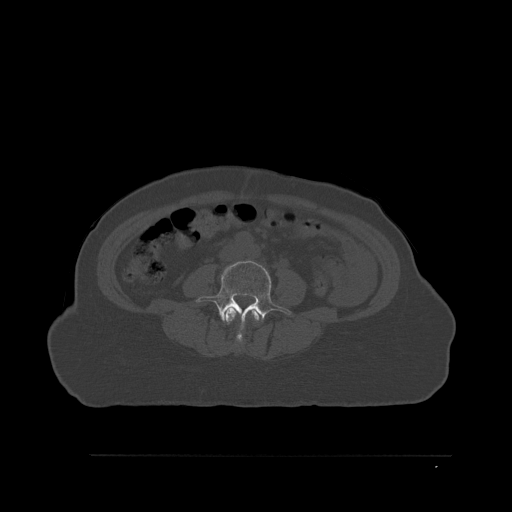
CT including the spine, one axial slice. Slice 211 of 527 in the series (ordered by position). Bone window (W 1800 / L 400 HU). 1.5 mm slice thickness. 512 × 512 image matrix. Patient: female, 73 years. Case-level facts recorded for this patient, not image findings: primary cancer: breast.
Structures marked on this image (semi-automatic segmentation, software-assisted and operator-edited):
- L3 vertebra: box from (x=224, y=307) to (x=260, y=344) px
- L4 vertebra: (x=196, y=260)–(x=291, y=335)